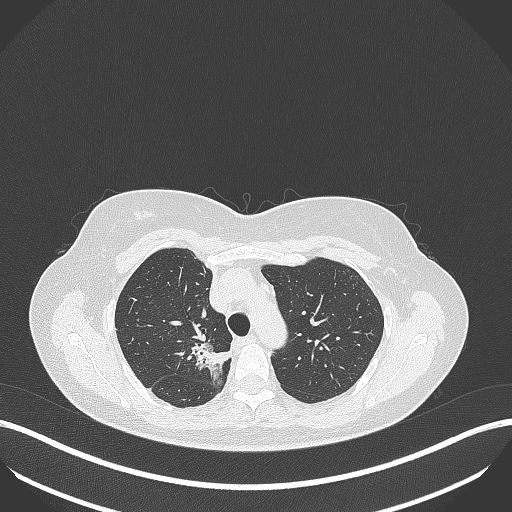
Chest CT, one axial slice. Position 295 of 386 along the scan axis. Reconstruction kernel B70f. Lung window (W 1500 / L -600 HU). 1 mm slice thickness. 512 × 512 image matrix, field of view 400 × 400 mm. Patient: female, 65 years. From the clinical record (not read from this slice): clinical TNM (as recorded): T1b N0 M0.
Outlined on this slice (bounding box drawn by a radiologist):
- lung tumour (recorded histology: adenocarcinoma): bounding box [x1, y1, x2, y2] px = [188, 339, 233, 386]